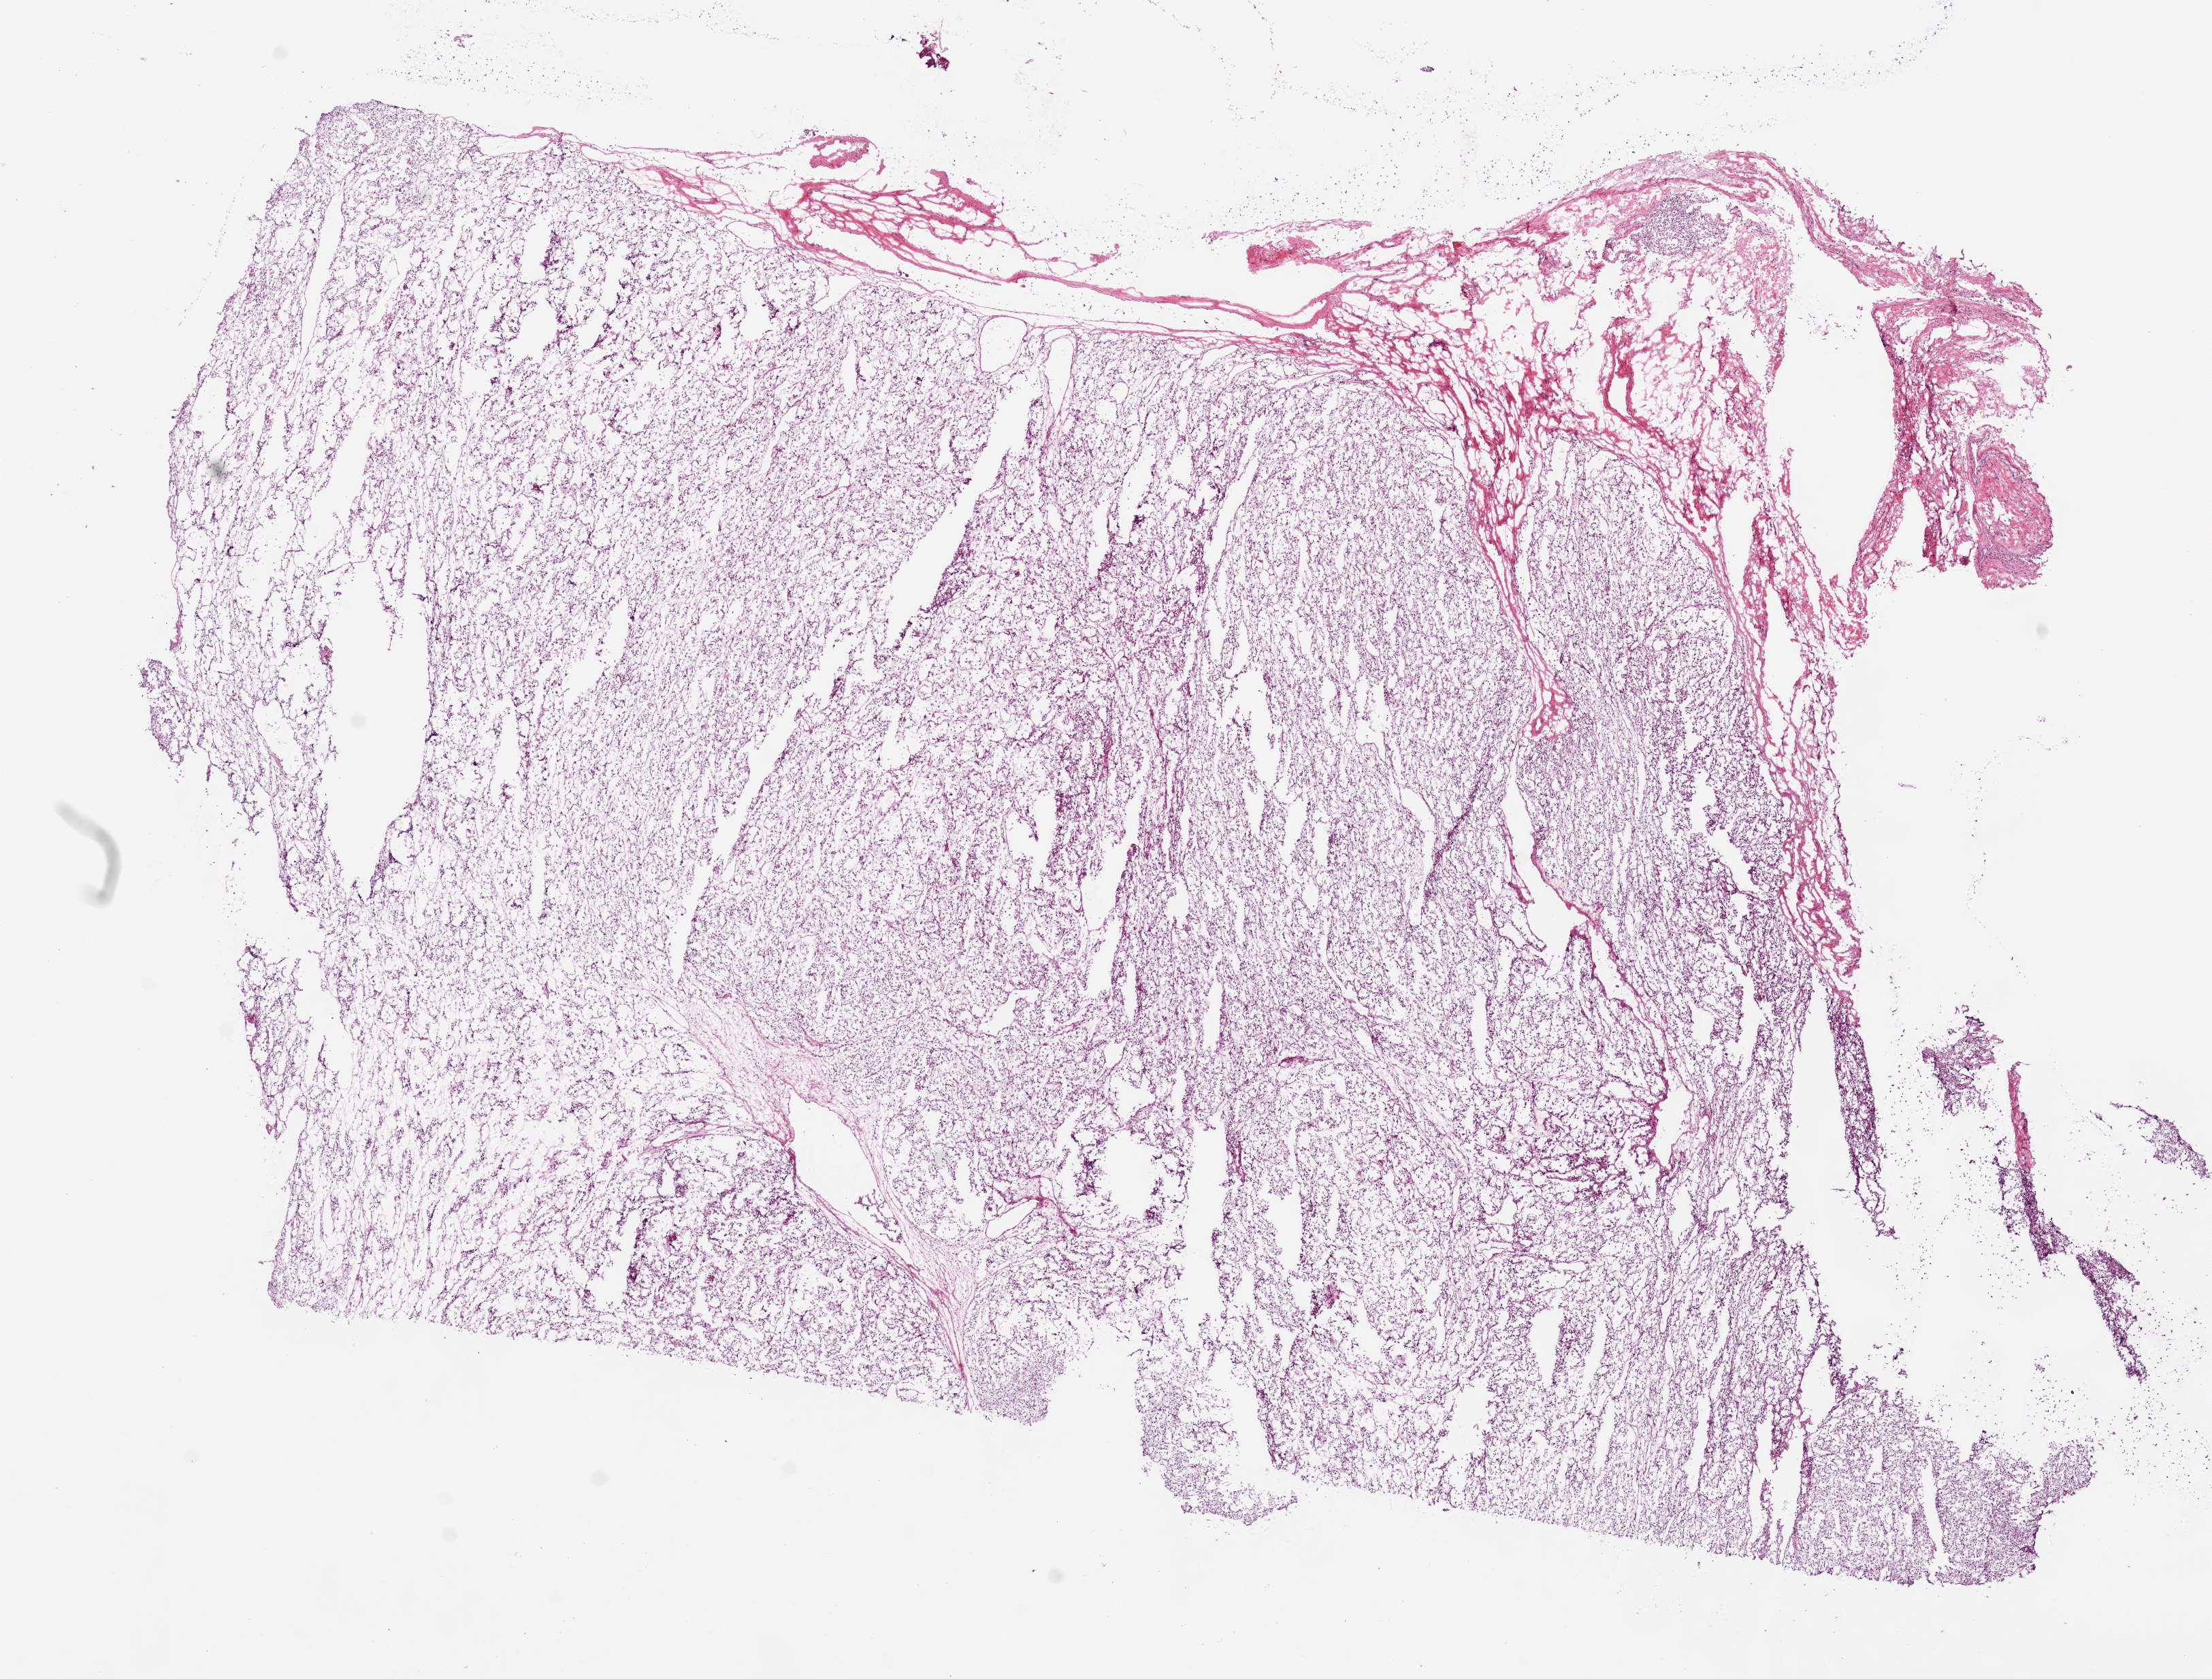
Hematoxylin and eosin (H&E) stained whole-slide image — low-resolution overview of the scanned area, about 13.0 x 9.9 mm (acquisition: 20x scan); frozen section from the bottom of the tissue portion; sample: primary tumour, kidney. Female patient; age at initial diagnosis 61 years. Histologic grade: G2 (moderately differentiated). Pathologist review of this section (percent, as recorded): tumour cells 85%, tumour nuclei 85%, normal cells 0%, stromal cells 15%, necrosis 0%.
* diagnosis: Clear cell adenocarcinoma, NOS
* AJCC pathologic stage: I